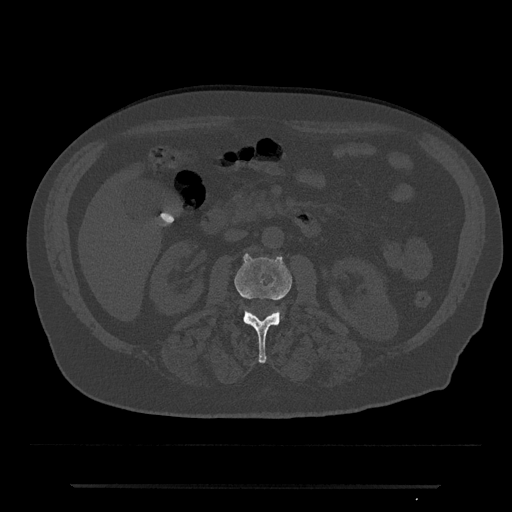
CT including the spine, one axial slice; slice 460 of 797 in the series (ordered by position); reconstruction kernel Br40s/3; bone window (W 1800 / L 400 HU); 0.5 mm slice thickness; 512 × 512 image matrix. Male patient, age 80 years. From the clinical record (not read from this slice): primary cancer: prostate; vertebrae with lytic lesions (as recorded): L1, T11.
Annotated regions visible in this slice (semi-automatically segmented with operator editing):
- L2 vertebra: box from (x=234, y=253) to (x=292, y=363) px